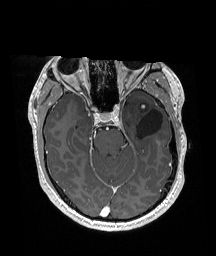
Brain MRI from a brain-tumour surgery series, one axial slice; position 115 of 192 along the scan axis; T1-weighted post-contrast; 216 × 256 image matrix. Case-level facts recorded for this patient, not image findings: histopathology: Glioneuronal tumor; WHO grade: 2; tumour location: Left Superior Temporal Gyrus.
Outlined on this slice (manually delineated by an expert):
- previous resection cavity: box from (x=137, y=109) to (x=163, y=138) px
- tumour: (x=141, y=104)–(x=147, y=110)